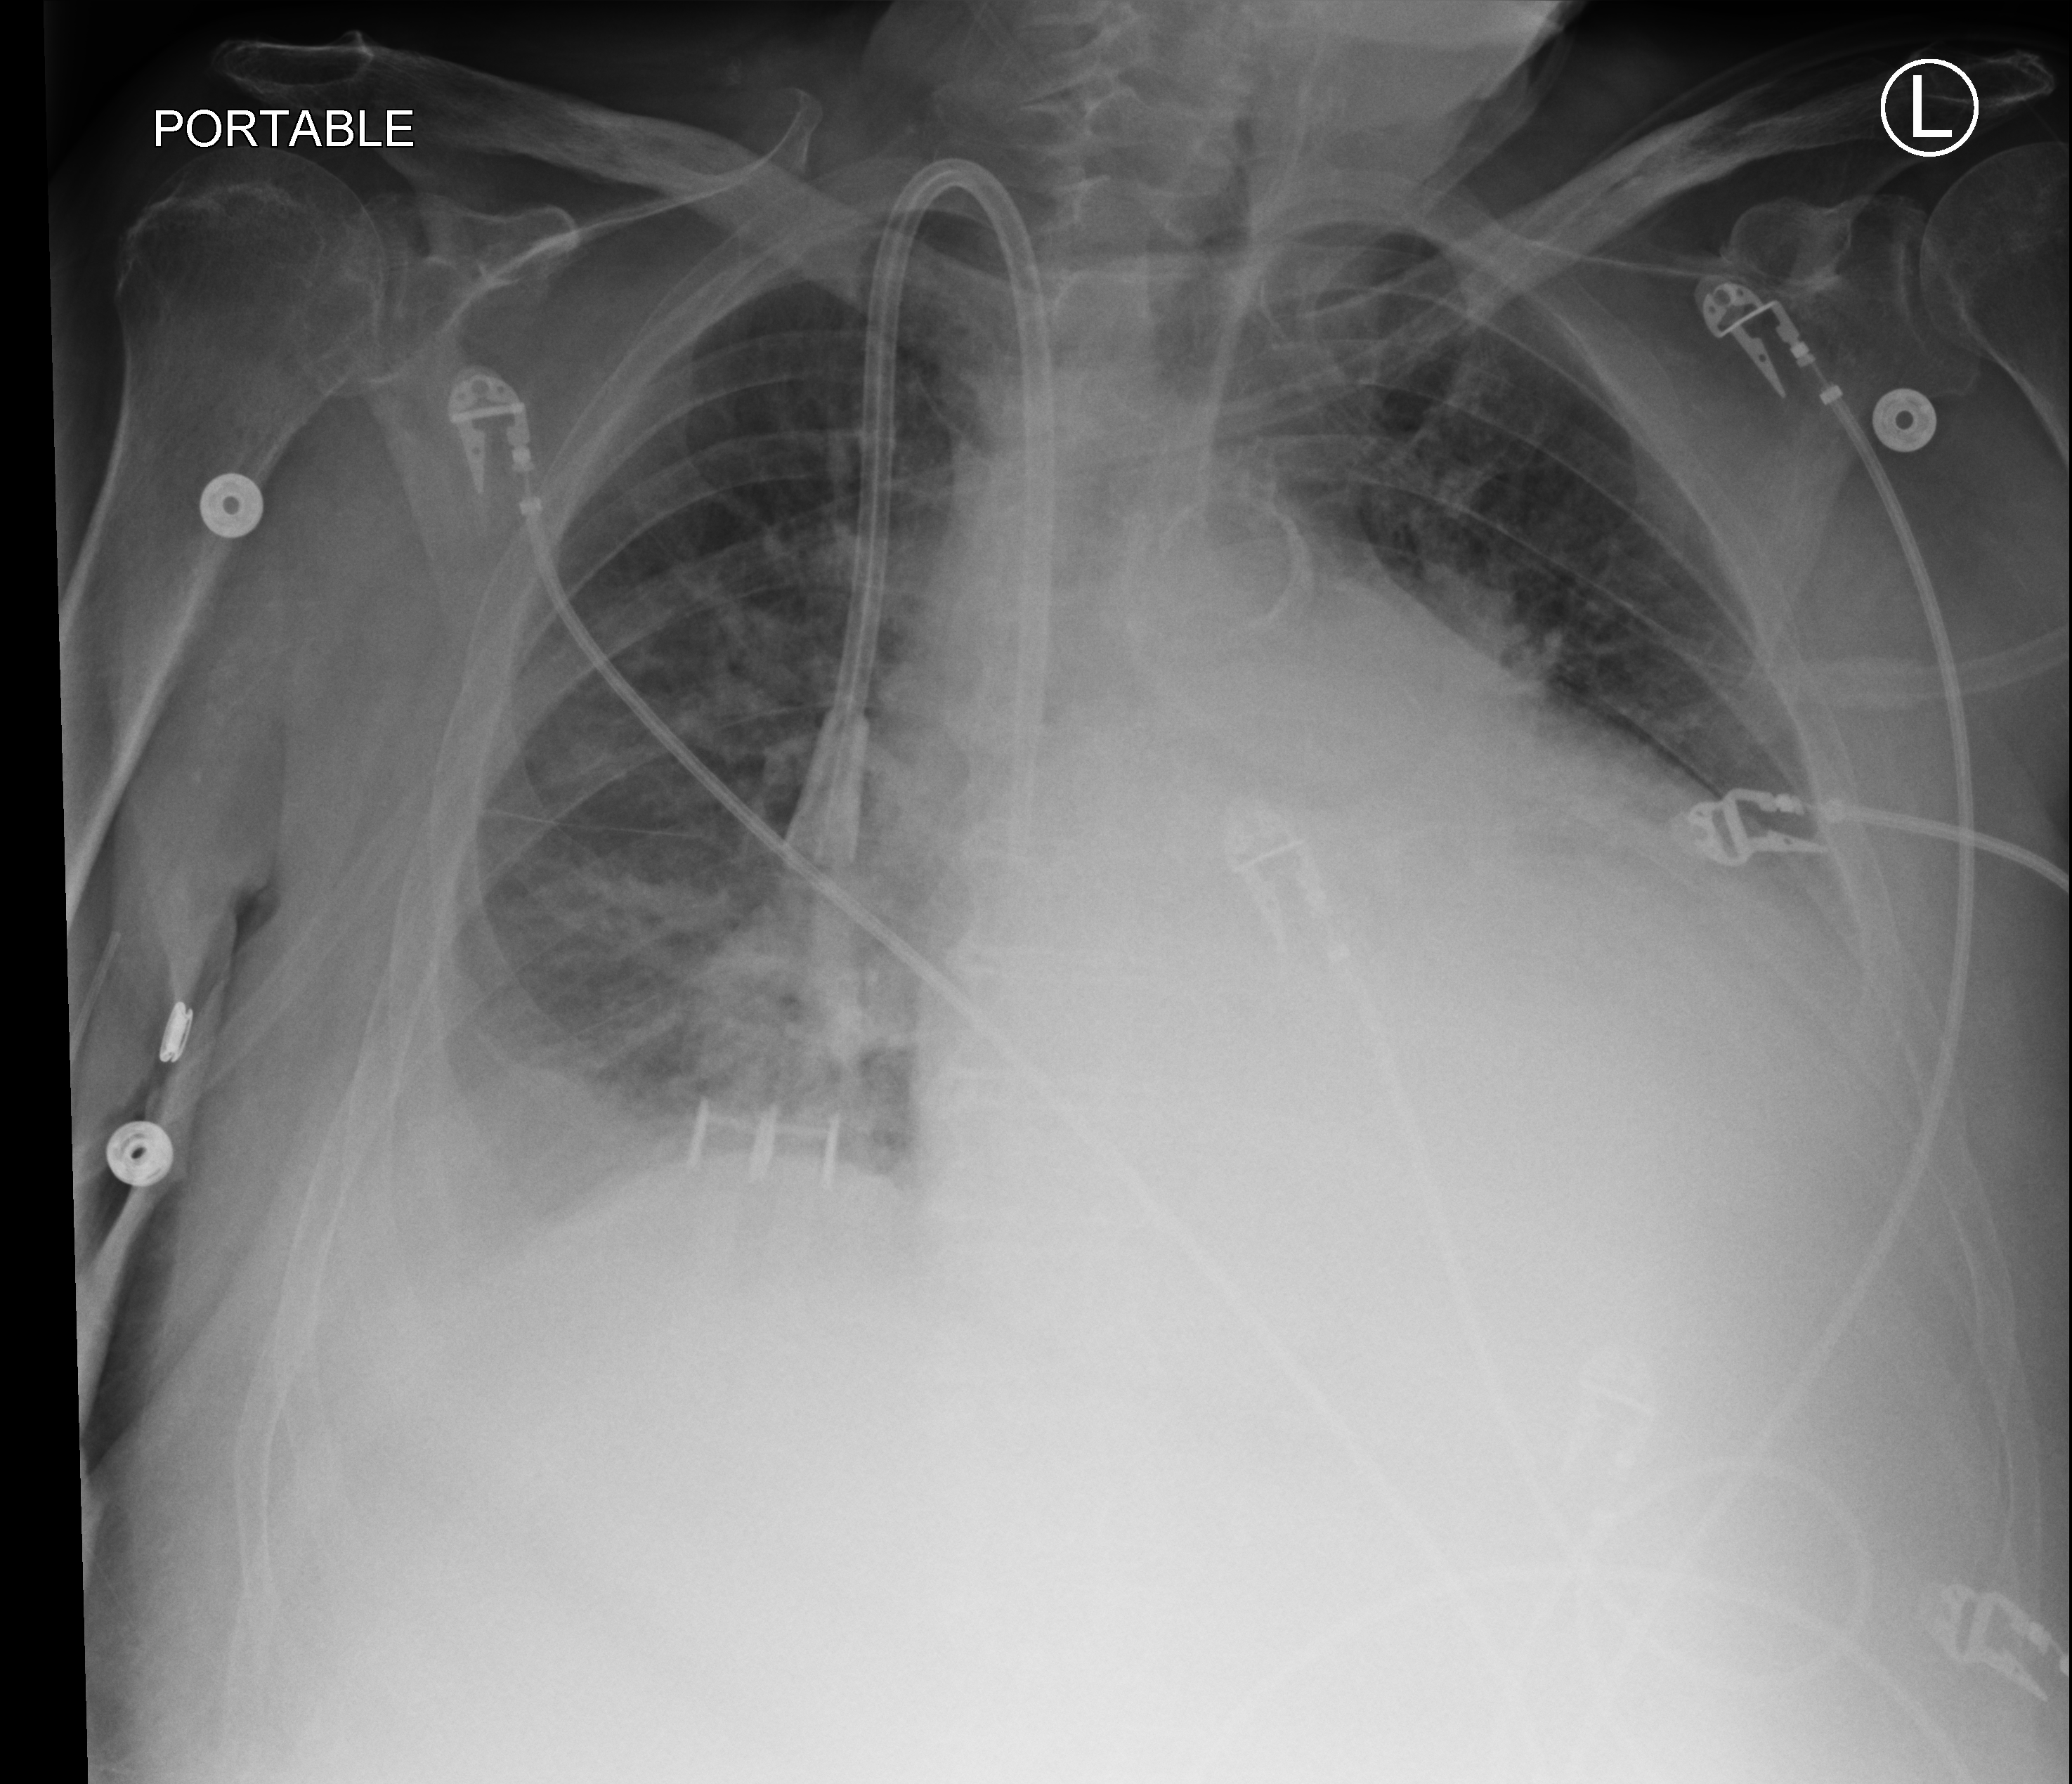
Chest X-ray (portable); anteroposterior (AP) projection. Patient hospitalised with COVID-19; male, aged 60–74 years.
Admission-level facts for this patient (not findings on this image; timing relative to this image not recorded):
- mechanically ventilated during this hospital stay: no
- hypertension (admission record): yes